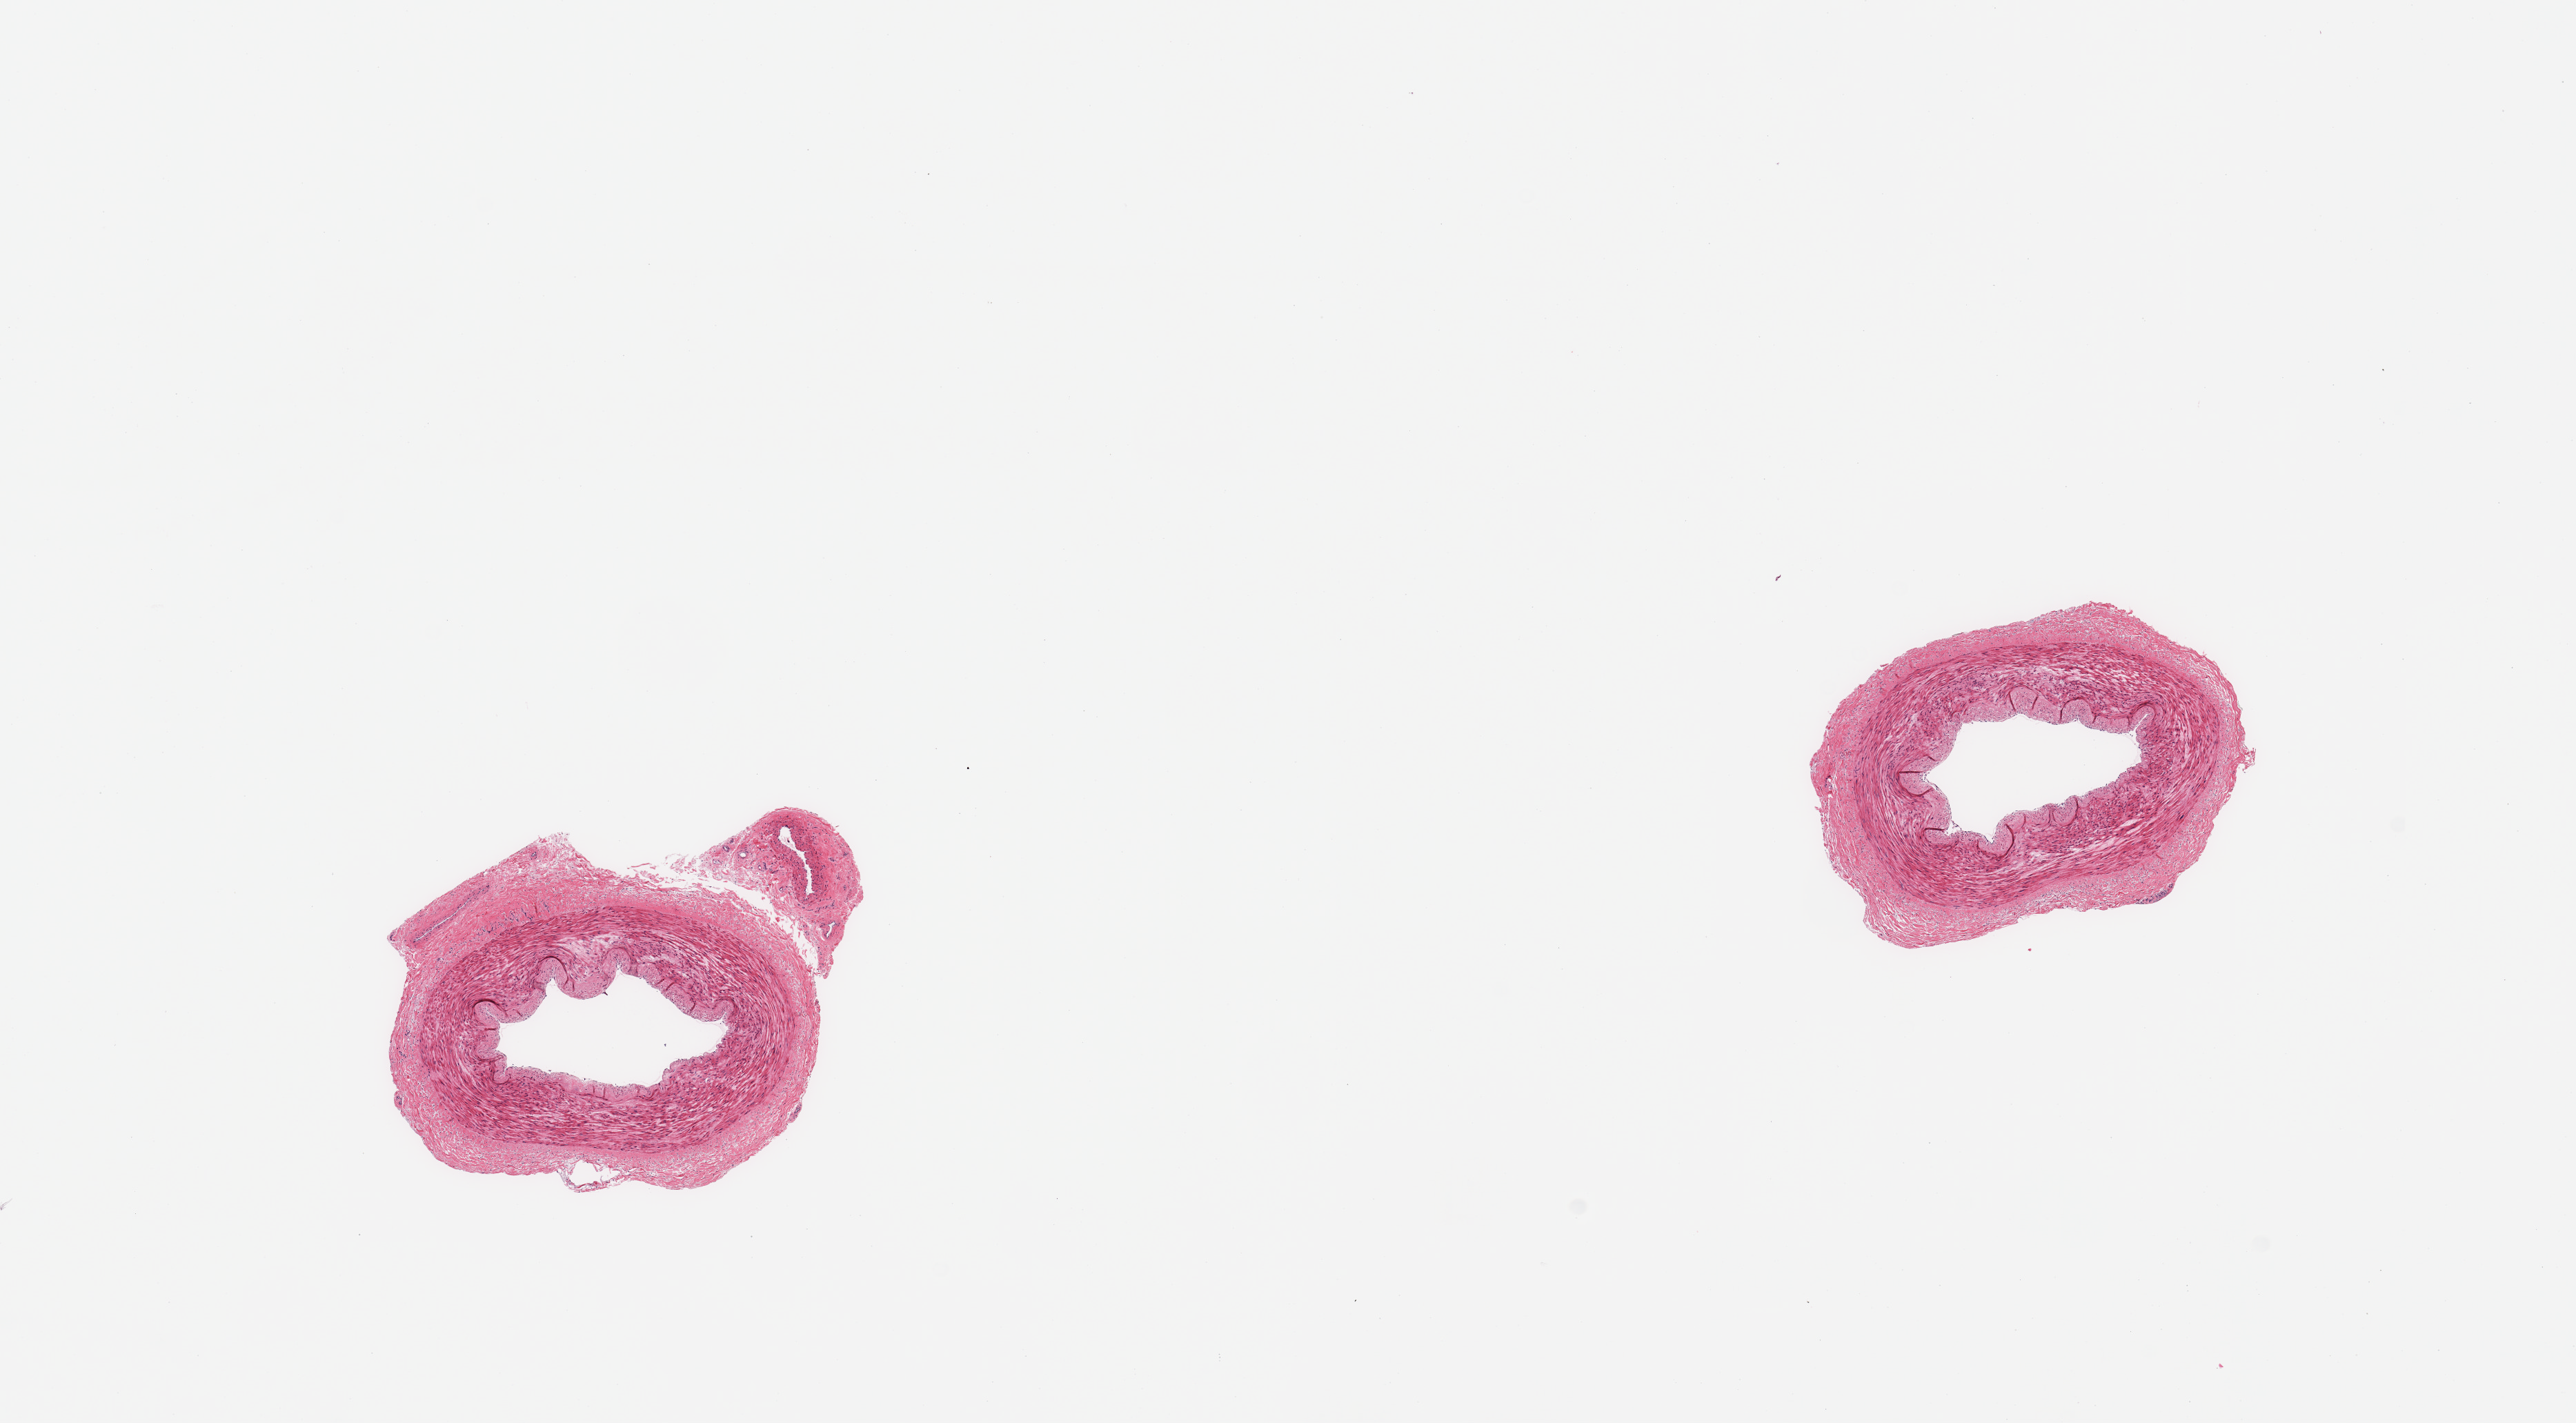
Haematoxylin and eosin whole-slide image, low-resolution overview of the scanned area, about 14.8 x 8.2 mm. PAXgene-fixed paraffin-embedded (PFPE) section. Section of tibial artery (target tissue). Tissue donor sample. Donor sex: male.
* reviewer comment on this tissue sample: 2 pieces; patent lumina and no plaque identified